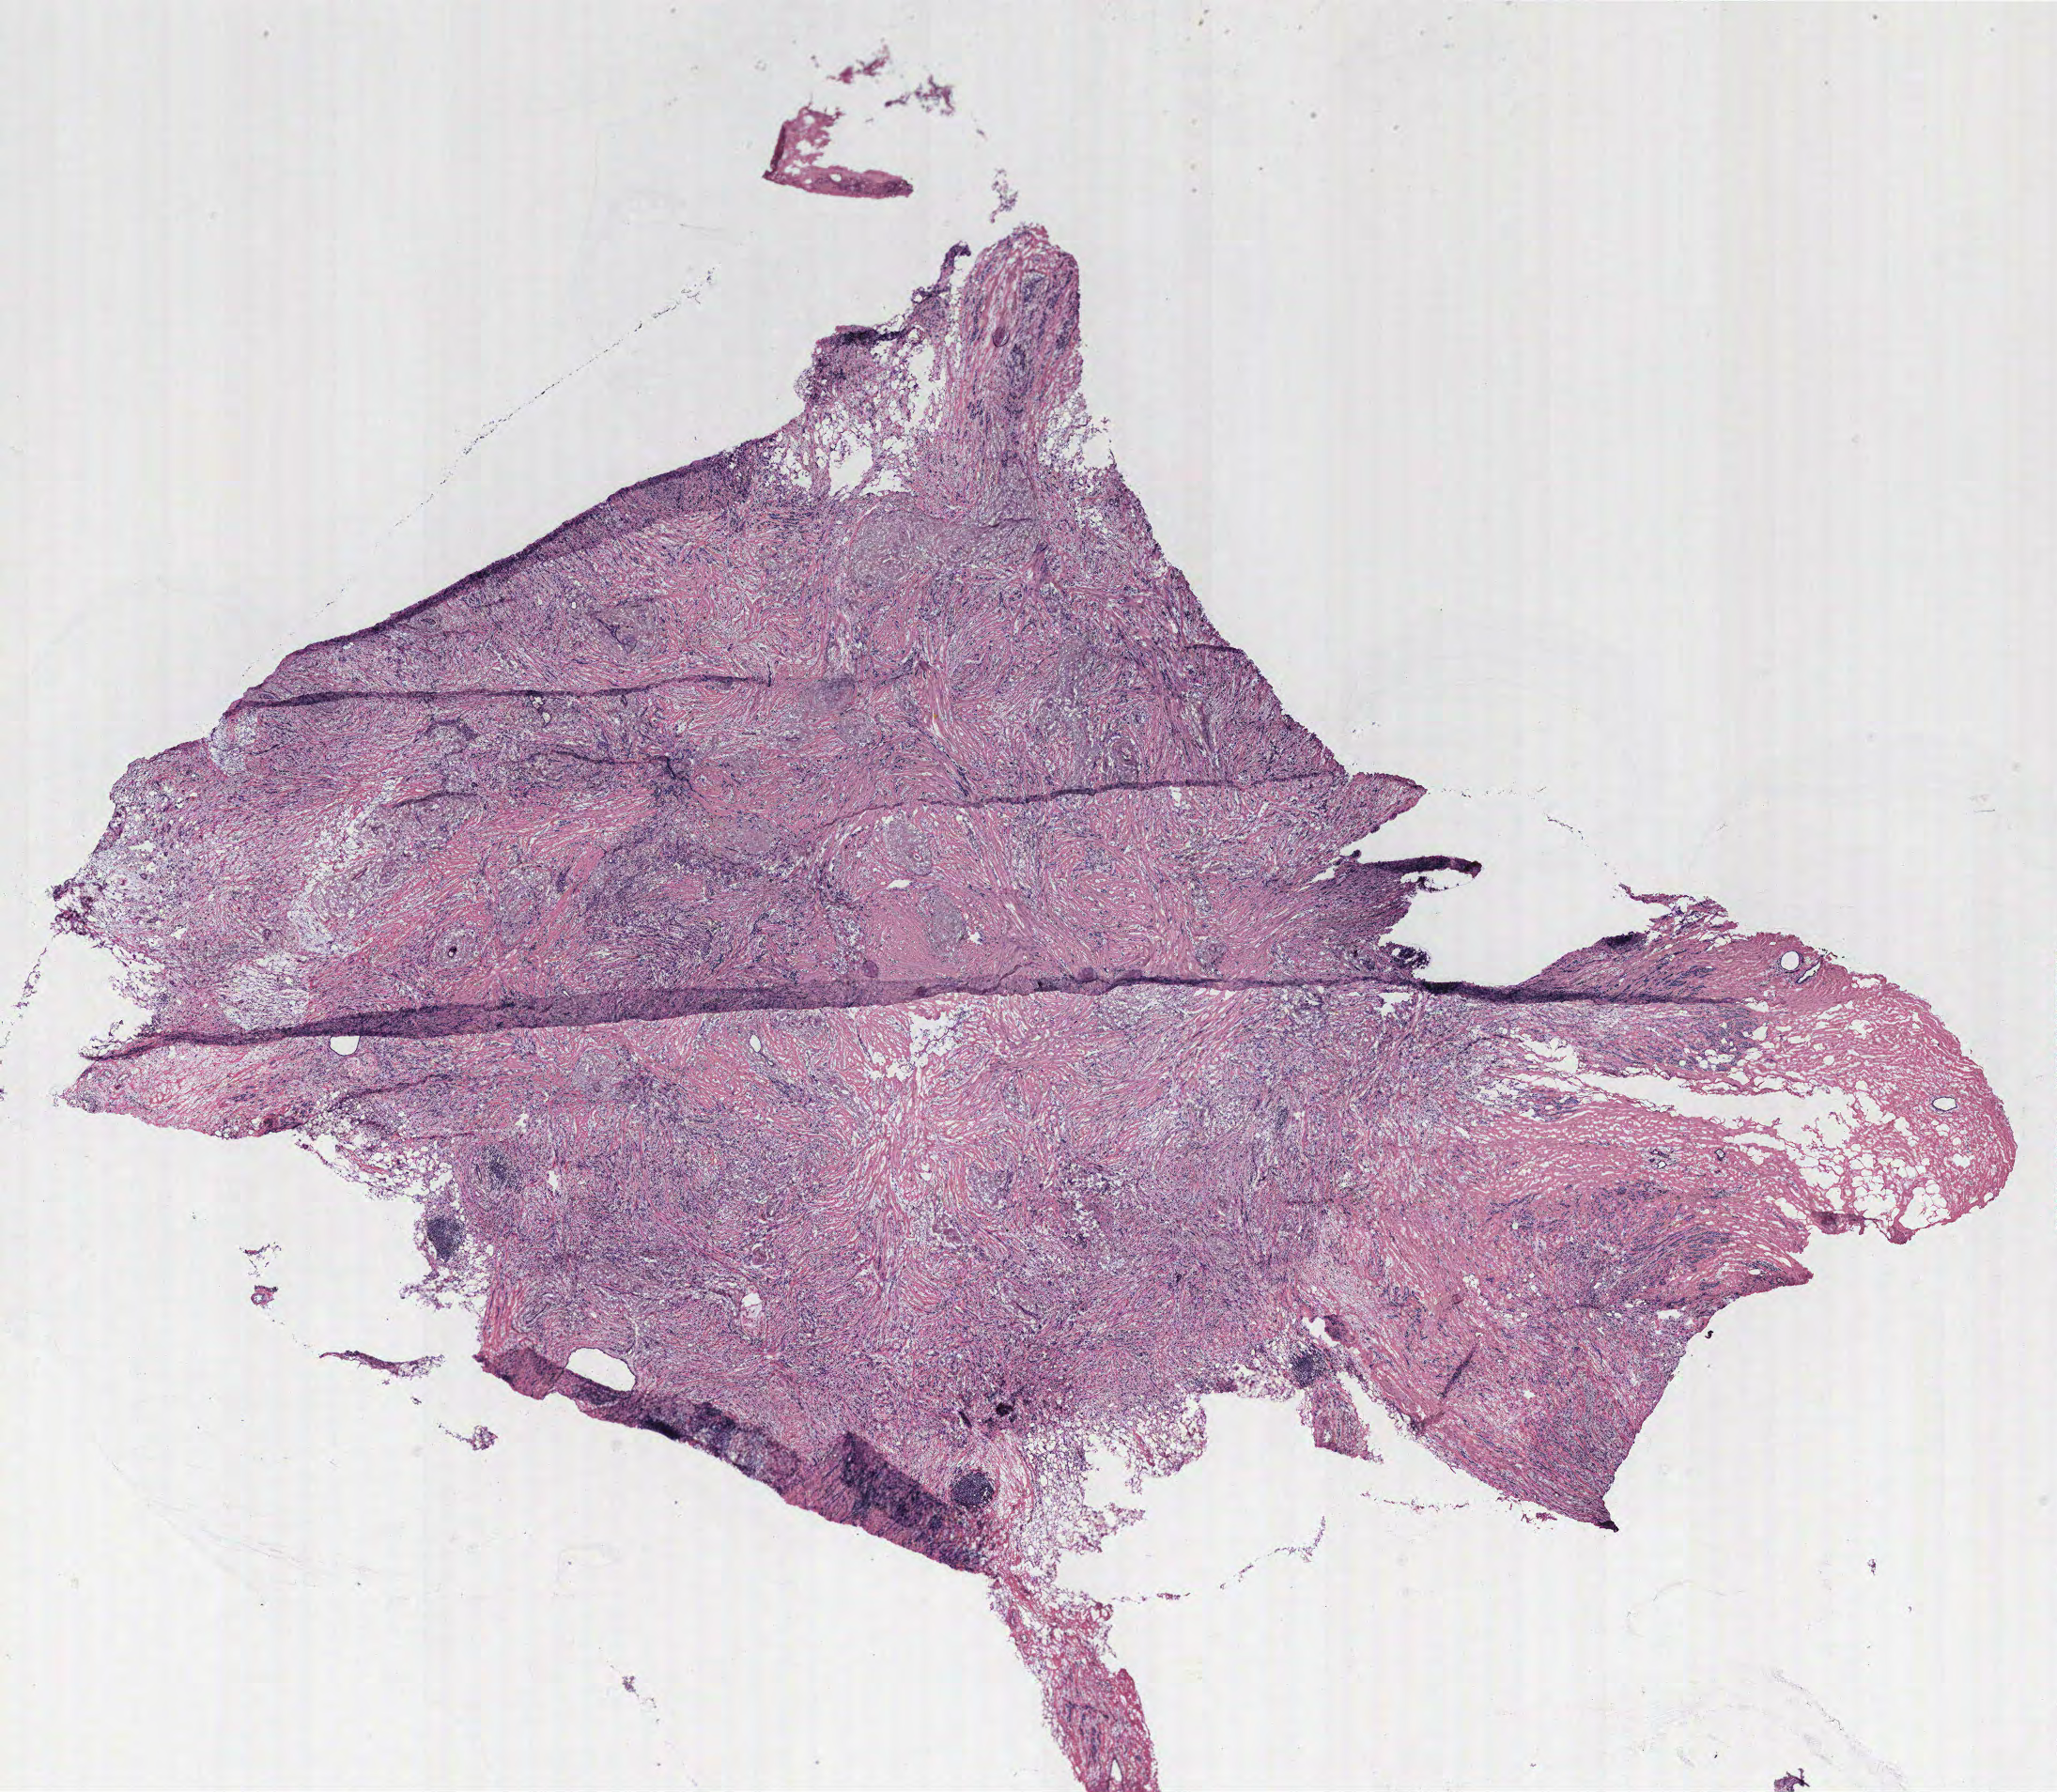
Hematoxylin and eosin (H&E) stained whole-slide image, whole scanned area (about 17.5 x 15.3 mm, from a 40x scan) shown as a low-resolution overview; breast, tissue type not recorded.
Patient diagnosis (cohort enrolment): breast cancer (breast).